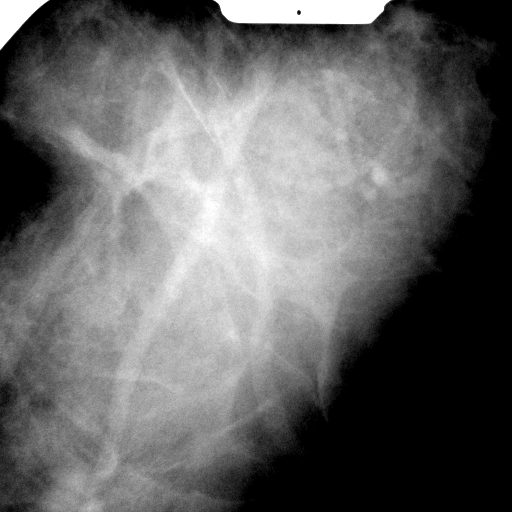
Spot-compression mammographic view.
Patient-level pathology facts (clinical record, not image findings): pathology diagnosis: benign fibroadenoma (right breast); pathology report notes: RIGHT BREAST CALCIFICATION WITH NEEDLE LOCATION: FIBROADENOMA (1.9CM). REMAINING BREAST TISSUE WITH ADENOSIS, FOCAL FIBROADENOMATOUS CHANGES, APOCRINE METAPLASIA, FIBROCYSTIC CHANGES, SMALL INTRADUCTAL PAPILLOMAS, AND USUAL TYPE DUCTAL HYPERPLASIA. MICROCALCIFICATIONS ASSOCIATED WITH BENIGN BREAST TISSUE ARE IDENTIFIED. NO IN-SITU OR INVASIVE CARCINOMA.